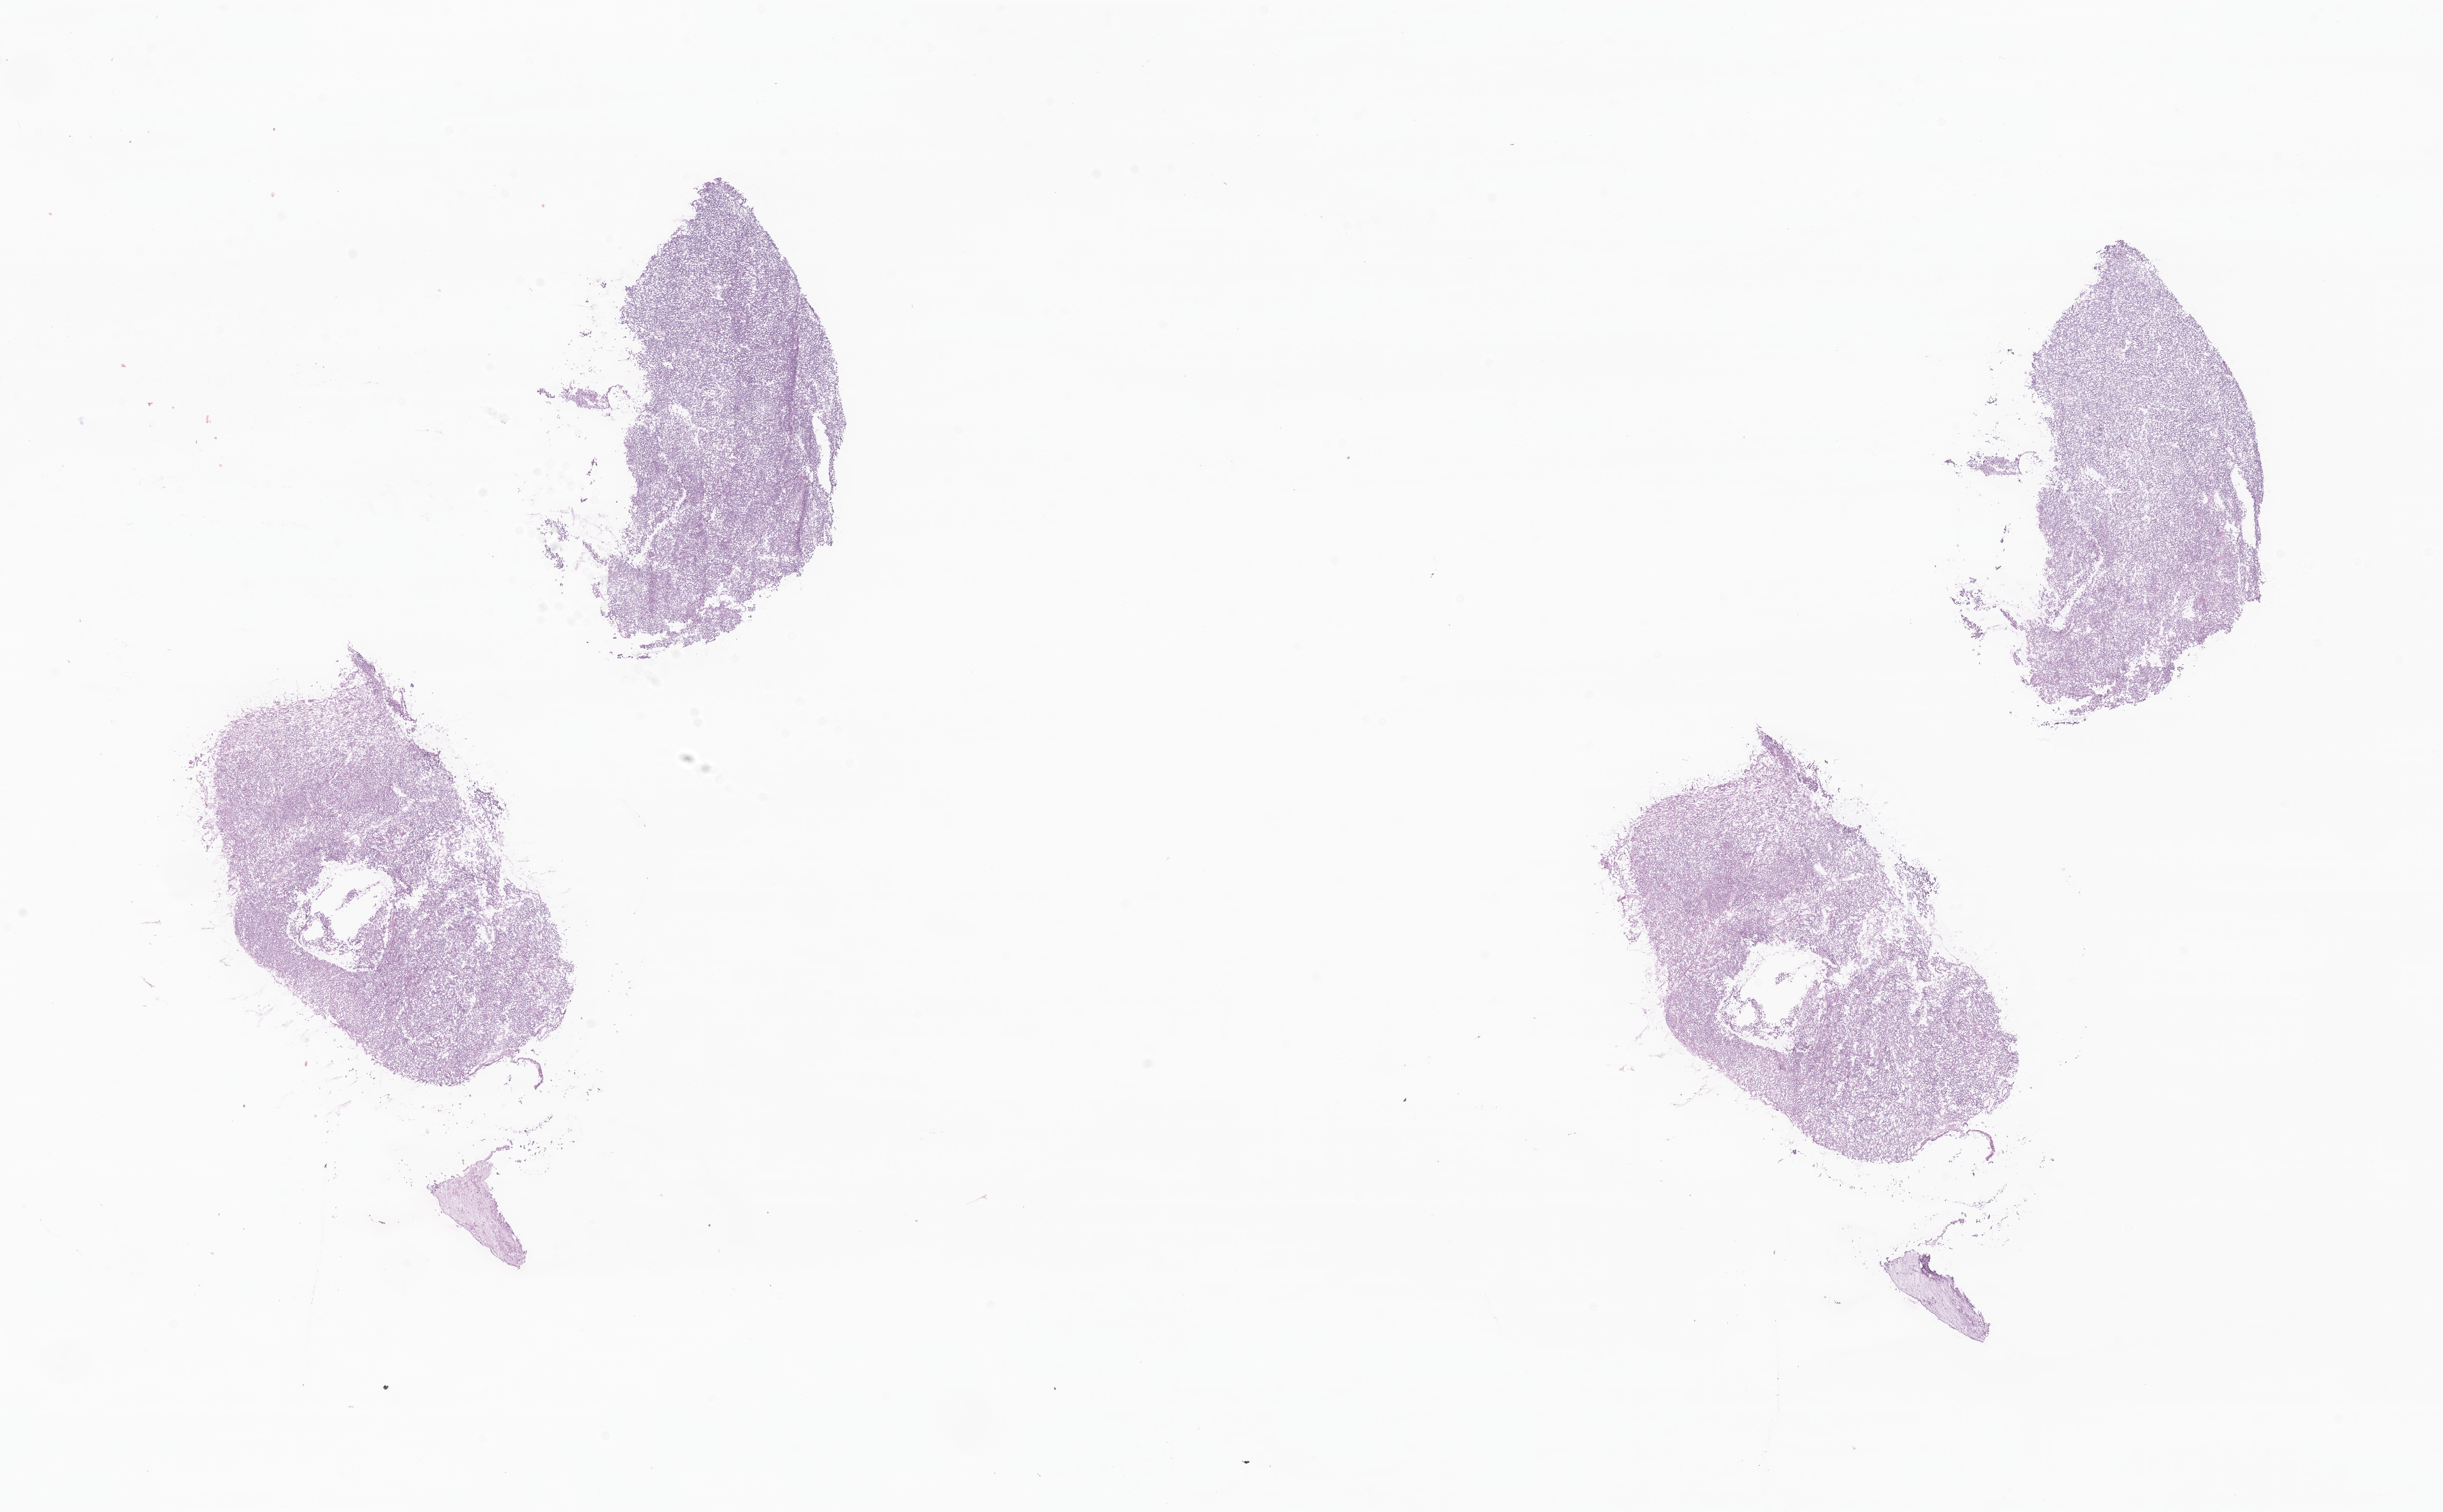
Whole-slide image, H&E stain of tumor tissue from the parietal lobe — low-resolution overview of the scanned area, about 25.0 x 15.5 mm; cryosection (OCT / tissue freezing medium). Patient: female, age 93 months (7 years 9 months).
Diagnosis (ICD-O-3 morphology term): Ependymoma, NOS.